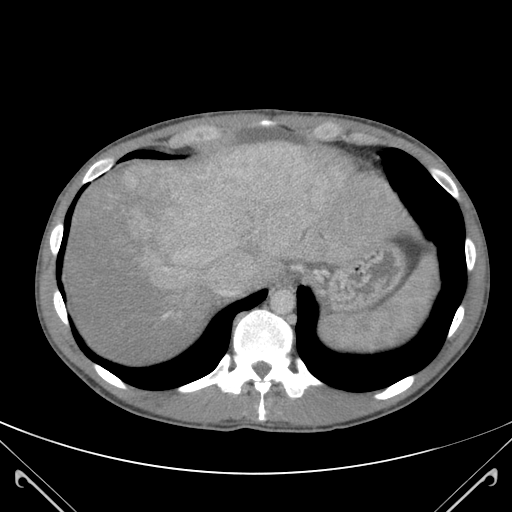
Contrast-enhanced abdominal CT (liver protocol), one axial slice; position 99 of 118 along the scan axis; soft-tissue window (W 400 / L 40 HU); 512 × 512 image matrix, field of view 380 × 380 mm. From the clinical record (not read from this slice): diagnosis: hepatocellular carcinoma (patient treated with transarterial chemoembolisation; whether this scan precedes or follows treatment is not stated here); TNM stage (as recorded): Stage-IIIB; Child-Pugh class: A; tumour nodularity: uninodular.
Annotated regions visible in this slice (semi-automatically segmented with operator editing):
- abdominal aorta: box from (x=273, y=289) to (x=295, y=312) px
- liver parenchyma outside the tumour (the mass and vessels are separate outlines, so this box may not span the whole liver): (x=71, y=151)–(x=352, y=360)
- mass: (x=95, y=142)–(x=339, y=300)
- liver vessels: (x=164, y=268)–(x=250, y=317)